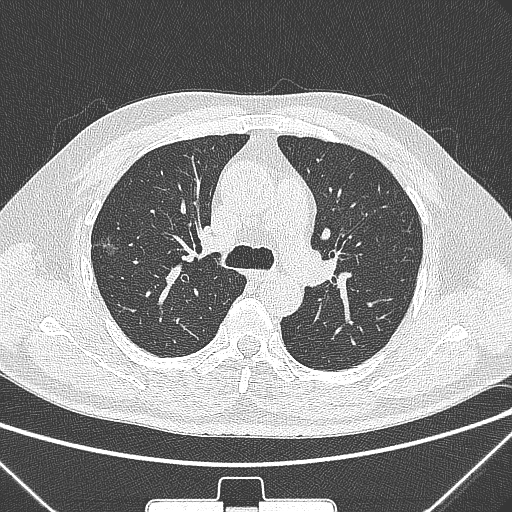
Chest CT, one axial slice; slice 204 of 320 in the series (ordered by position); 120 kVp; lung window (W 1500 / L -600 HU); 512 × 512 image matrix, field of view 350 × 350 mm. Male patient, age 58 years. From the clinical record (not read from this slice): clinical TNM (as recorded): T1c N0 M0; histopathological grade: G2.
Outlined on this slice (rectangle marked by the reading radiologist):
- lung tumour (recorded histology: adenocarcinoma): bounding box (x1, y1, x2, y2) in pixels: (93, 236, 123, 266)